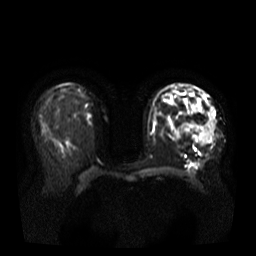
Breast MRI, one axial slice. Position 20 of 37 along the scan axis. Diffusion-weighted series; image 2 of 4 stored at this slice position (different b-values; order by instance number). 3 T. 5 mm slice thickness. 256 × 256 image matrix, field of view 380 × 380 mm. Female patient.
Structures marked on this image (manually delineated by an expert):
- tumour on diffusion-weighted imaging: bounding box (x1, y1, x2, y2) in pixels: (185, 107, 215, 145)